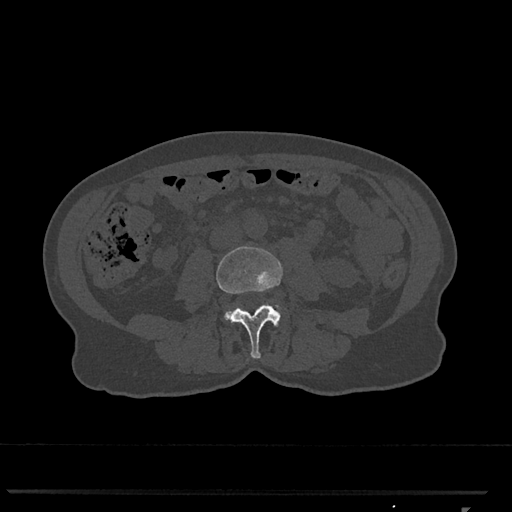
CT including the spine, one axial slice. Position 256 of 793 along the scan axis. Bone window (W 1800 / L 400 HU). 0.5 mm slice thickness. 512 × 512 image matrix. Female patient, age 62 years. Case-level facts recorded for this patient, not image findings: primary cancer: renal.
Structures marked on this image (semi-automatically segmented with operator editing):
- L3 vertebra: bounding box [x1, y1, x2, y2] px = [216, 246, 283, 359]
- L4 vertebra: [225, 305, 279, 319]